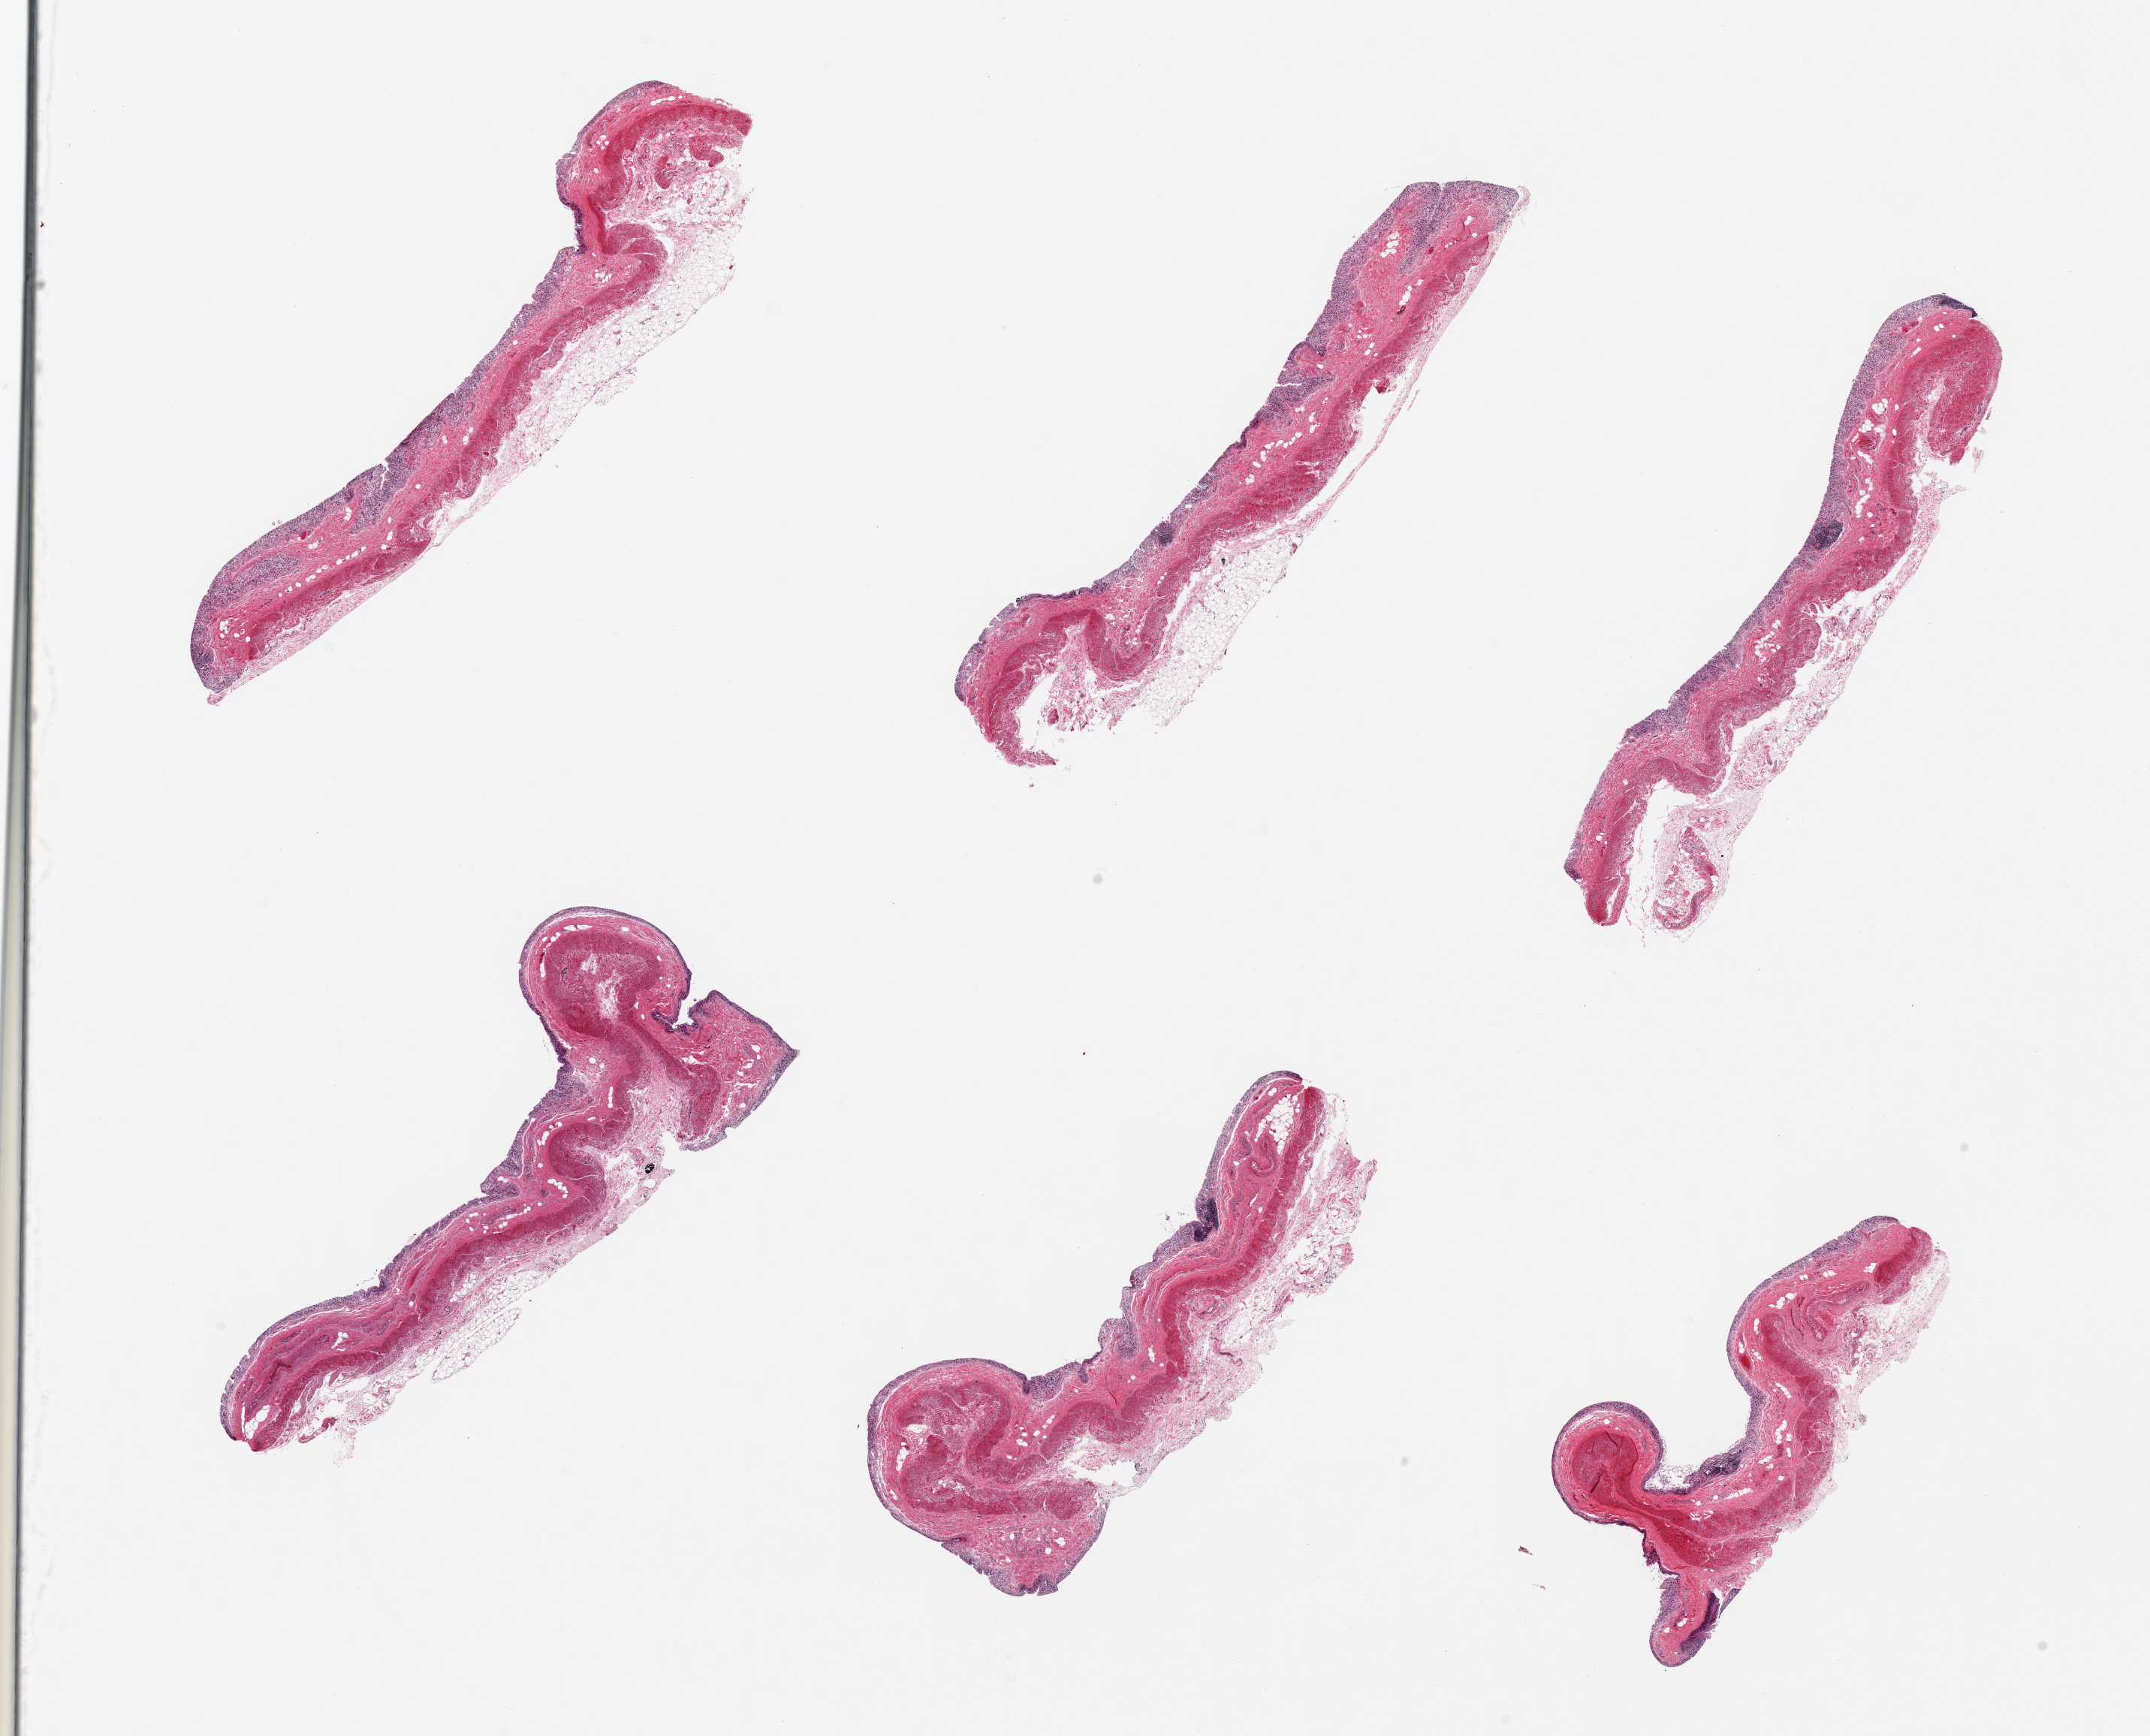
H&E whole-slide image, whole scanned area (about 22.6 x 18.3 mm) shown as a low-resolution overview; PAXgene-fixed paraffin-embedded (PFPE) section; sampled site (target tissue): transverse colon; donor tissue sample.
Review note (as recorded): 6 pieces; mucosa = autolysis 3; muscle = 2.